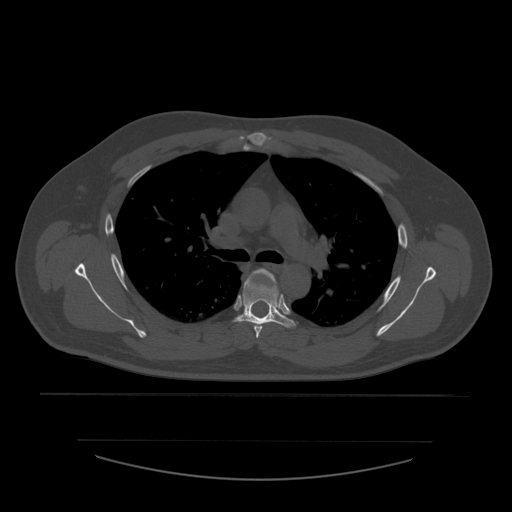
CT including the spine, one axial slice; position 403 of 532 along the scan axis; reconstruction kernel STANDARD; 120 kVp; bone window (W 1800 / L 400 HU); 1.25 mm slice thickness; 512 × 512 image matrix, field of view 441 × 441 mm. Patient age 44 years. From the clinical record (not read from this slice): primary cancer: soft tissue sarcoma.
Outlined on this slice (semi-automatic segmentation, software-assisted and operator-edited):
- T4 vertebra: bounding box (x1, y1, x2, y2) in pixels: (253, 269, 278, 338)
- T5 vertebra: (234, 269, 295, 328)